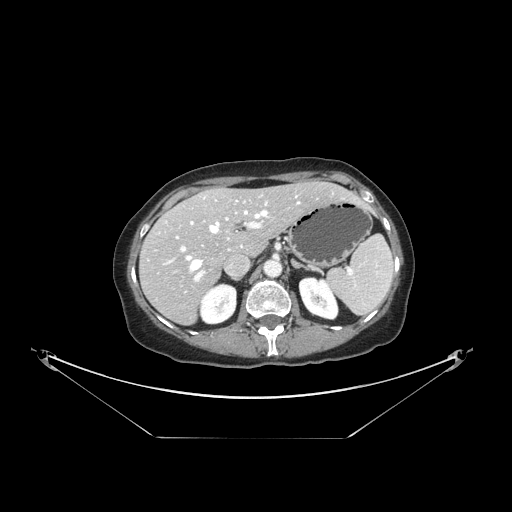
Contrast-enhanced abdominal CT, one axial slice; slice 96 of 148 in the series (ordered by position); reconstruction kernel STANDARD; 120 kVp; soft-tissue window (W 400 / L 40 HU); 2.5 mm slice thickness; 512 × 512 image matrix, field of view 500 × 500 mm. Female patient, age 73 years. Case-level facts recorded for this patient, not image findings: diagnosis: colorectal cancer liver metastases, imaged before liver resection; multiple liver metastases: no; largest metastasis: 1 cm; disease in both lobes: no.
Annotated regions visible in this slice (expert manual segmentation):
- hepatic veins: bounding box [x1, y1, x2, y2] px = [186, 195, 300, 271]
- liver: [141, 182, 355, 323]
- planned liver remnant (the part of the liver to remain after resection): [169, 182, 356, 255]
- portal vein (with intrahepatic branches): [171, 204, 267, 282]